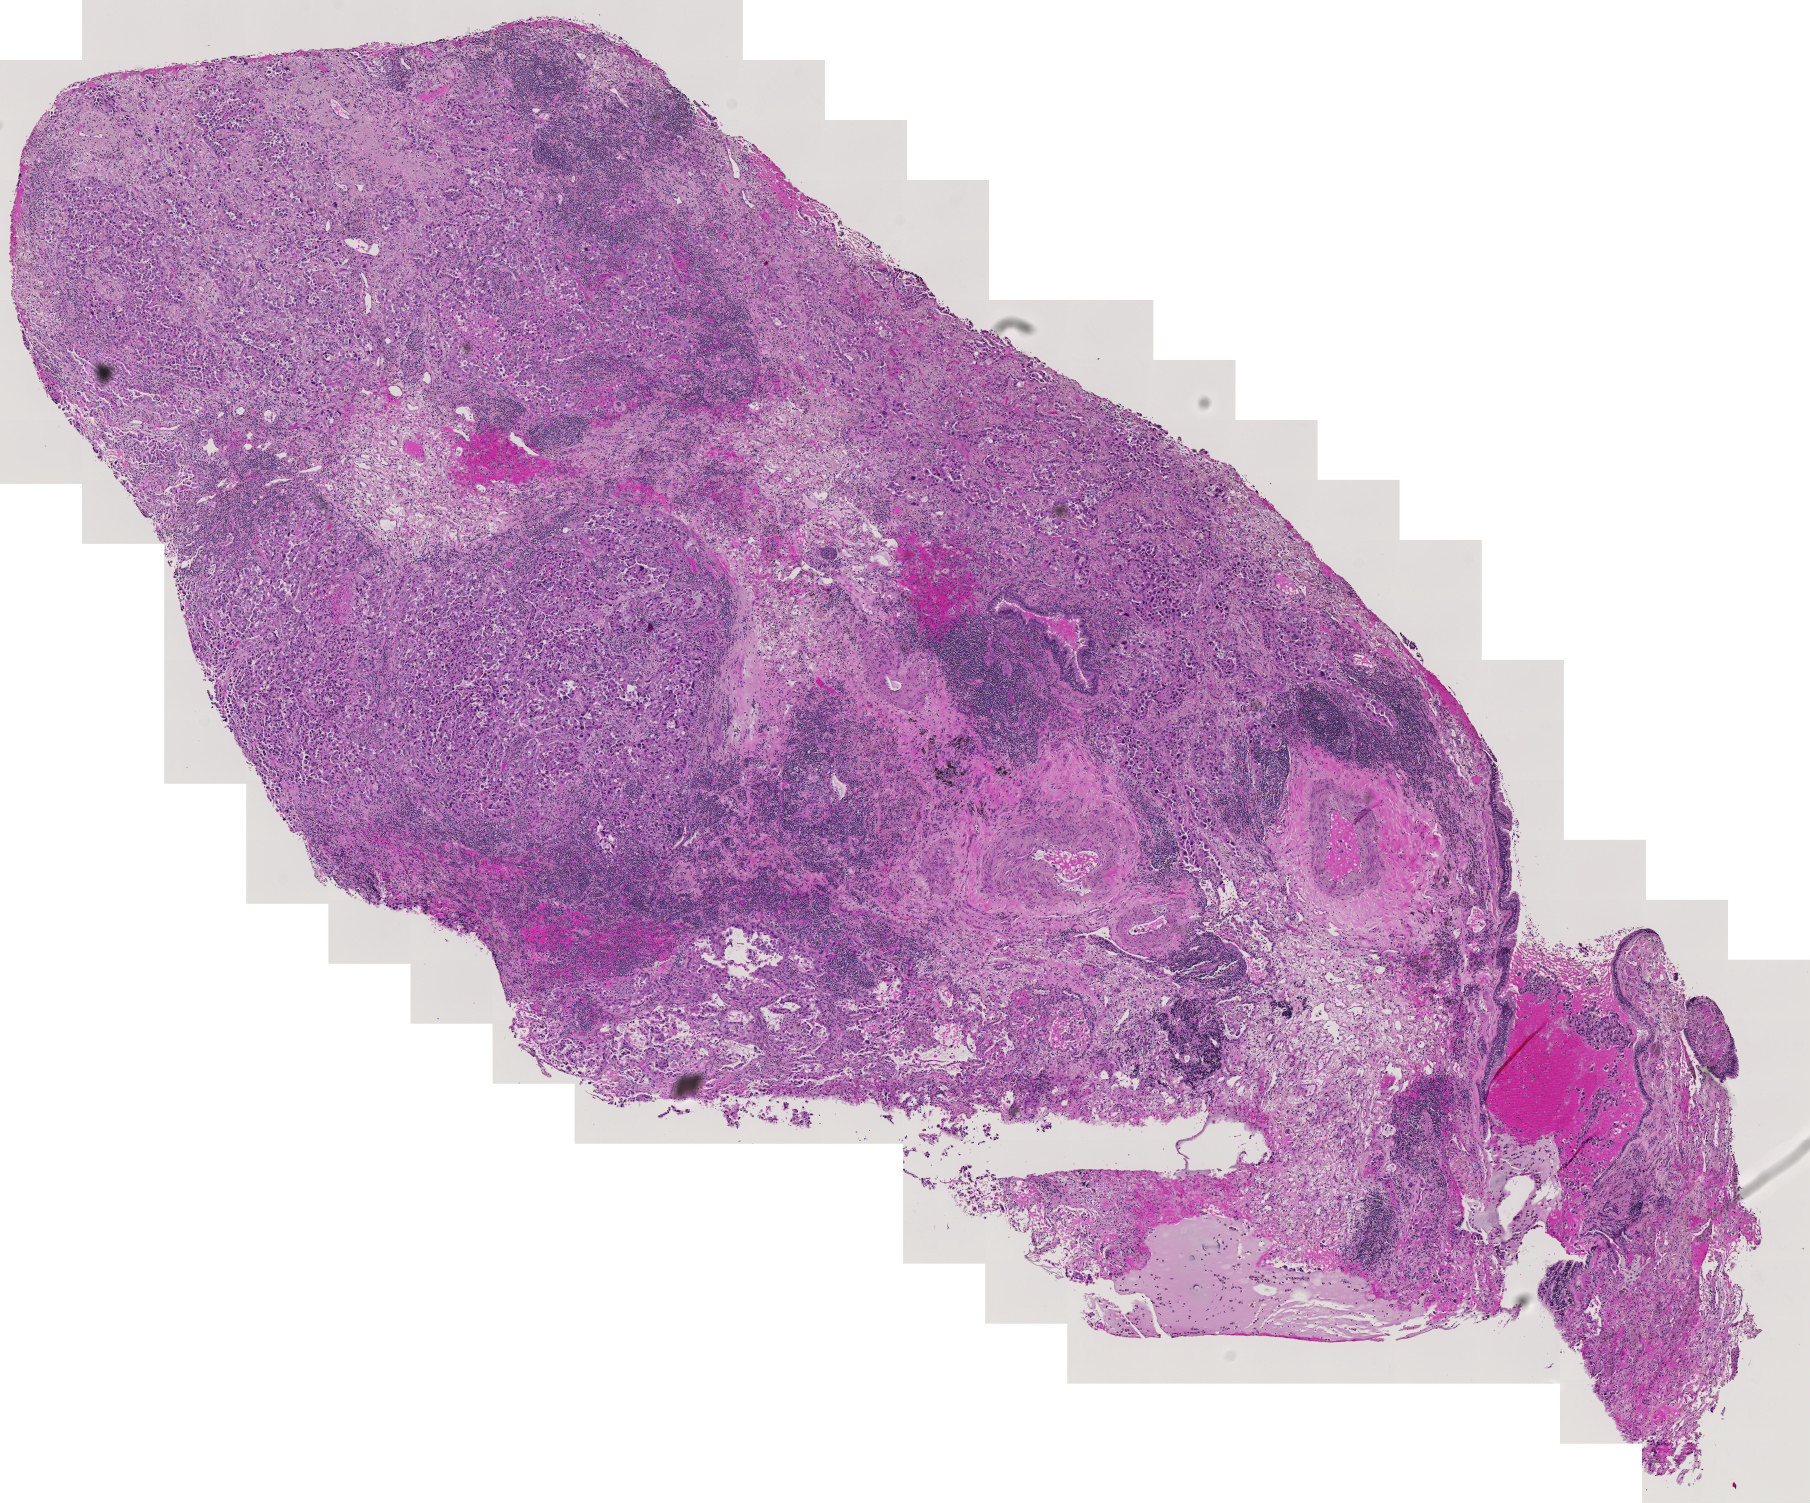
Whole-slide histology image, Hematoxylin and eosin (H&E) stained, shown as a low-resolution overview of the whole scanned area (about 9.4 x 7.8 mm). Tumour tissue sample, lung. Female, 68 y/o.
Histologic diagnosis: Adenocarcinoma, NOS.